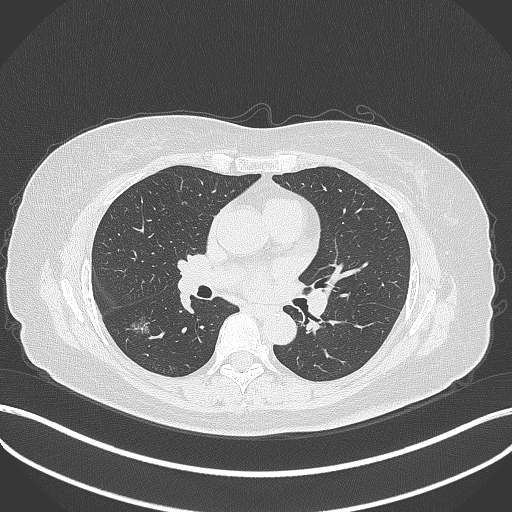
Chest CT, one axial slice; position 169 of 322 along the scan axis; 120 kVp; lung window (W 1500 / L -600 HU); 512 × 512 image matrix, field of view 400 × 400 mm. Patient: female, 64 years. From the clinical record (not read from this slice): clinical TNM (as recorded): T1c N0 M0; histopathological grade: G1.
Structures marked on this image (bounding box drawn by a radiologist):
- lung tumour (recorded histology: adenocarcinoma): bounding box [x1, y1, x2, y2] px = [125, 311, 151, 339]